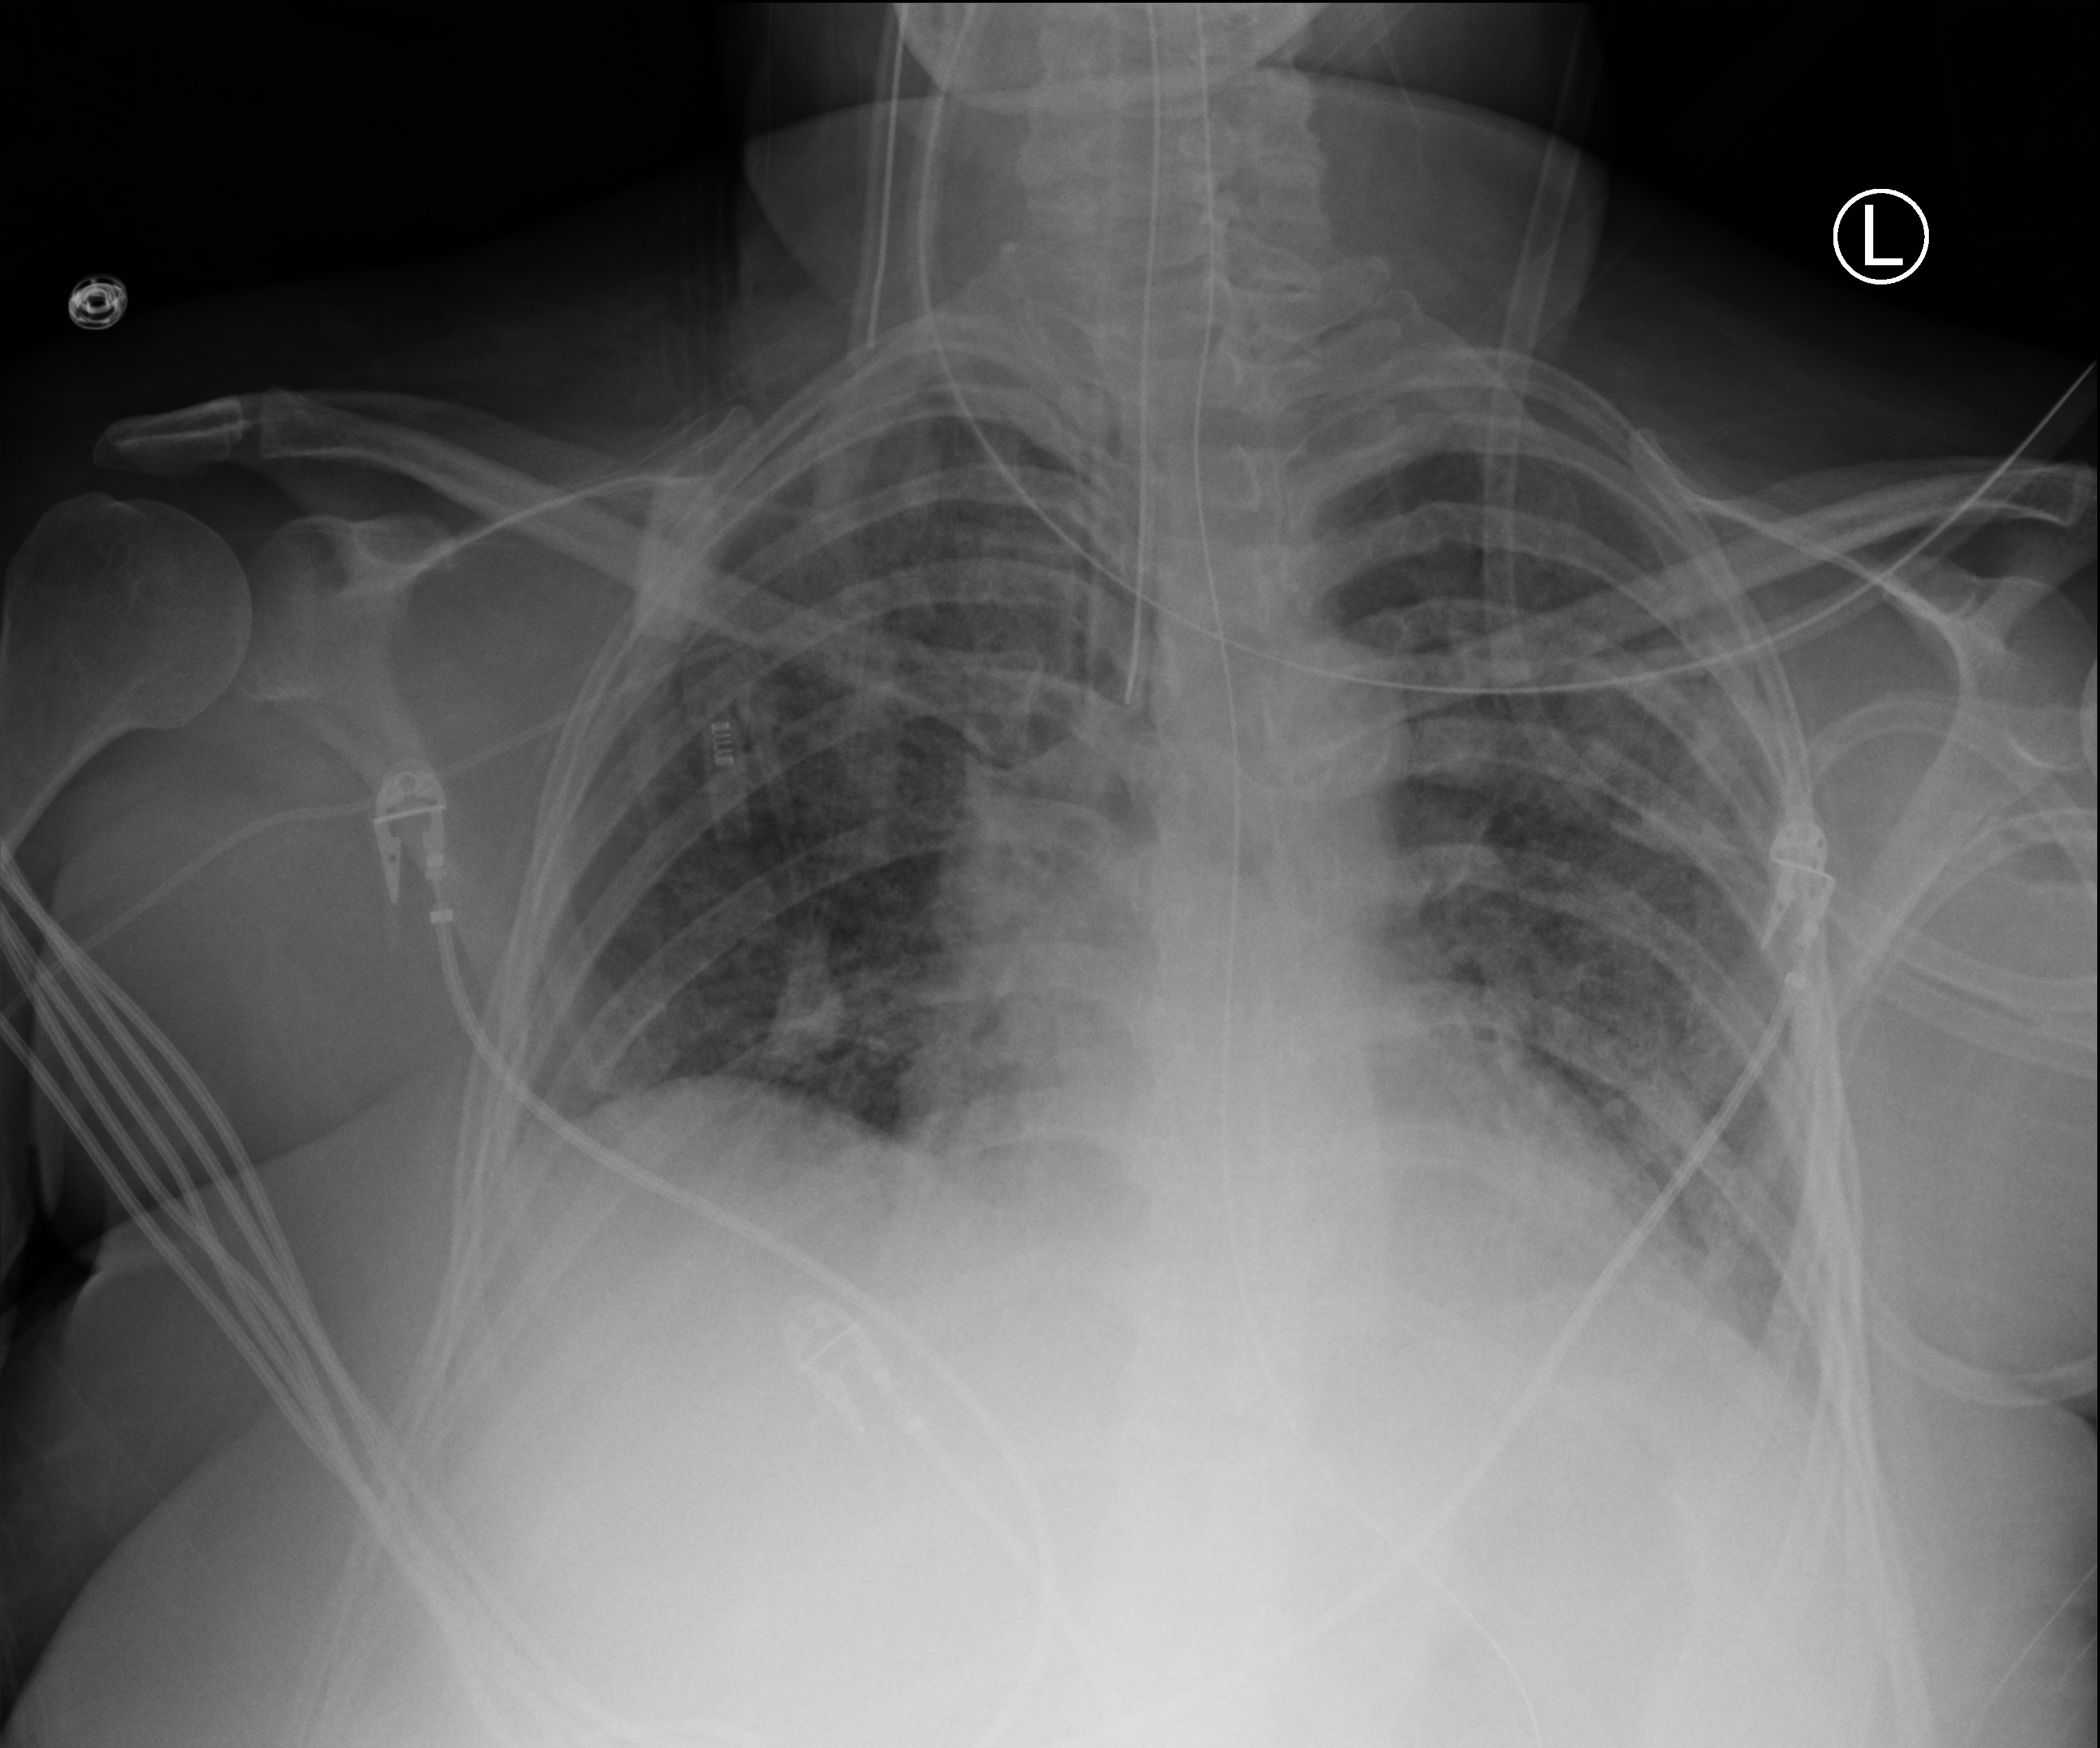
Bedside chest radiograph (computed radiography). Female patient hospitalised with COVID-19, age 18–59 years.
From the hospital-stay record, not from the radiograph (when in the stay this image was taken is not recorded):
- mechanically ventilated during this hospital stay: yes